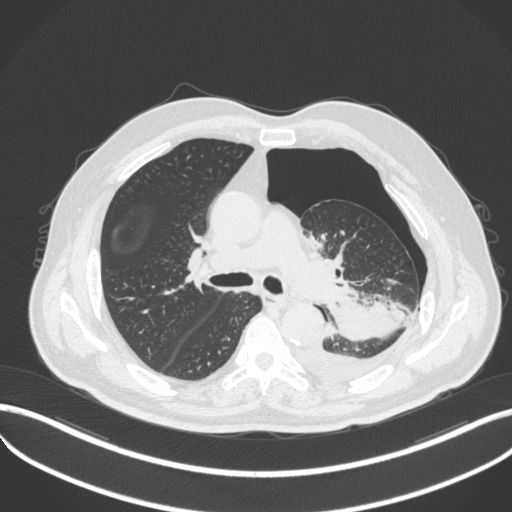
Chest CT, one axial slice. Position 321 of 466 along the scan axis. Reconstruction kernel B31f. 120 kVp. Lung window (W 1500 / L -600 HU). 512 × 512 image matrix. Patient: male, 76 years. Case-level facts recorded for this patient, not image findings: clinical TNM (as recorded): T3 N0 M1b.
Annotated regions visible in this slice (rectangle marked by the reading radiologist):
- lung tumour (recorded histology: adenocarcinoma): bounding box (x1, y1, x2, y2) in pixels: (323, 287, 403, 346)